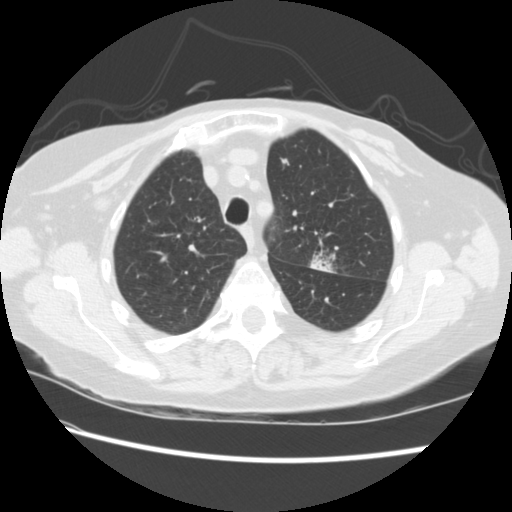
Low-dose screening chest CT, one axial slice. Slice 169 of 224 in the series (ordered by position). 120 kVp. Lung window (W 1500 / L -600 HU). 2.5 mm slice thickness. 512 × 512 image matrix, field of view 340 × 340 mm.
Structures marked on this image (outlined manually by an expert reader):
- lesion 1 (tumor, upper lobe of left lung): box from (x=310, y=254) to (x=333, y=273) px